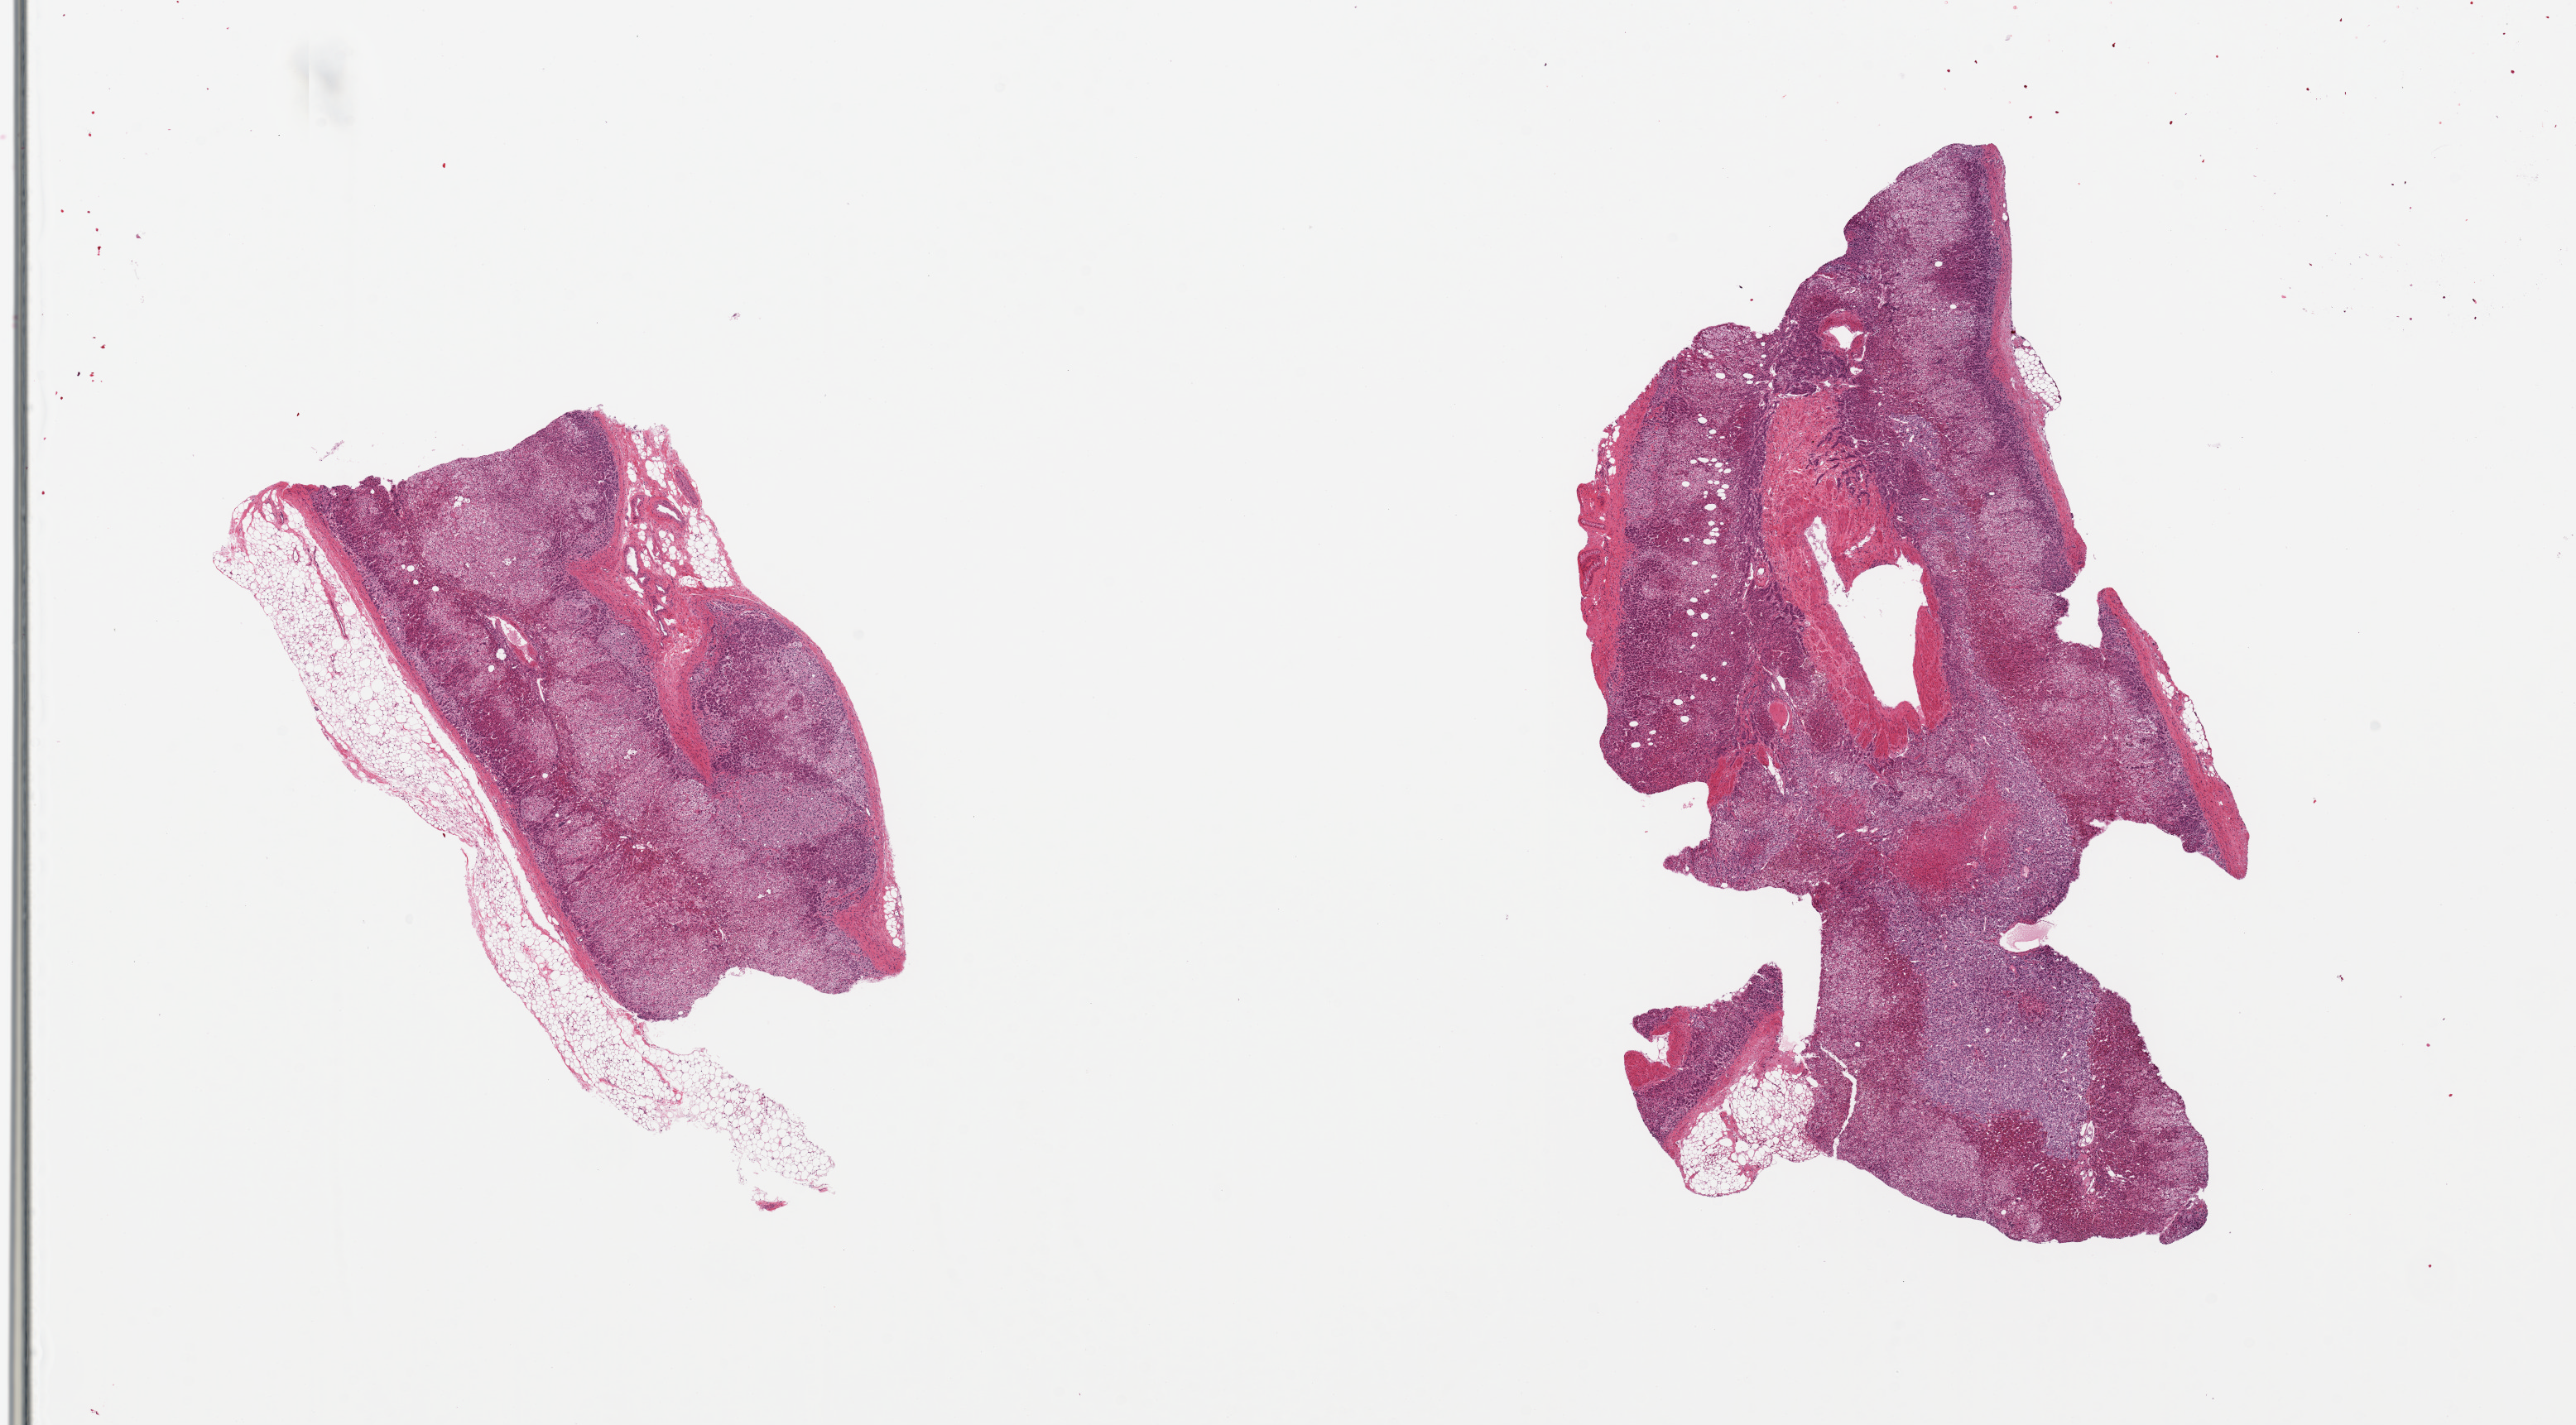
Whole-slide image, hematoxylin and eosin (H&E) stain, brightfield — shown as a low-resolution overview of the whole scanned area (about 24.6 x 13.6 mm); PAXgene-fixed, paraffin-embedded tissue; section of adrenal gland (target tissue); tissue donor sample. Donor: female.
Review note (as recorded): 2 pieces, smaller piece is ~20% adipose tissue.